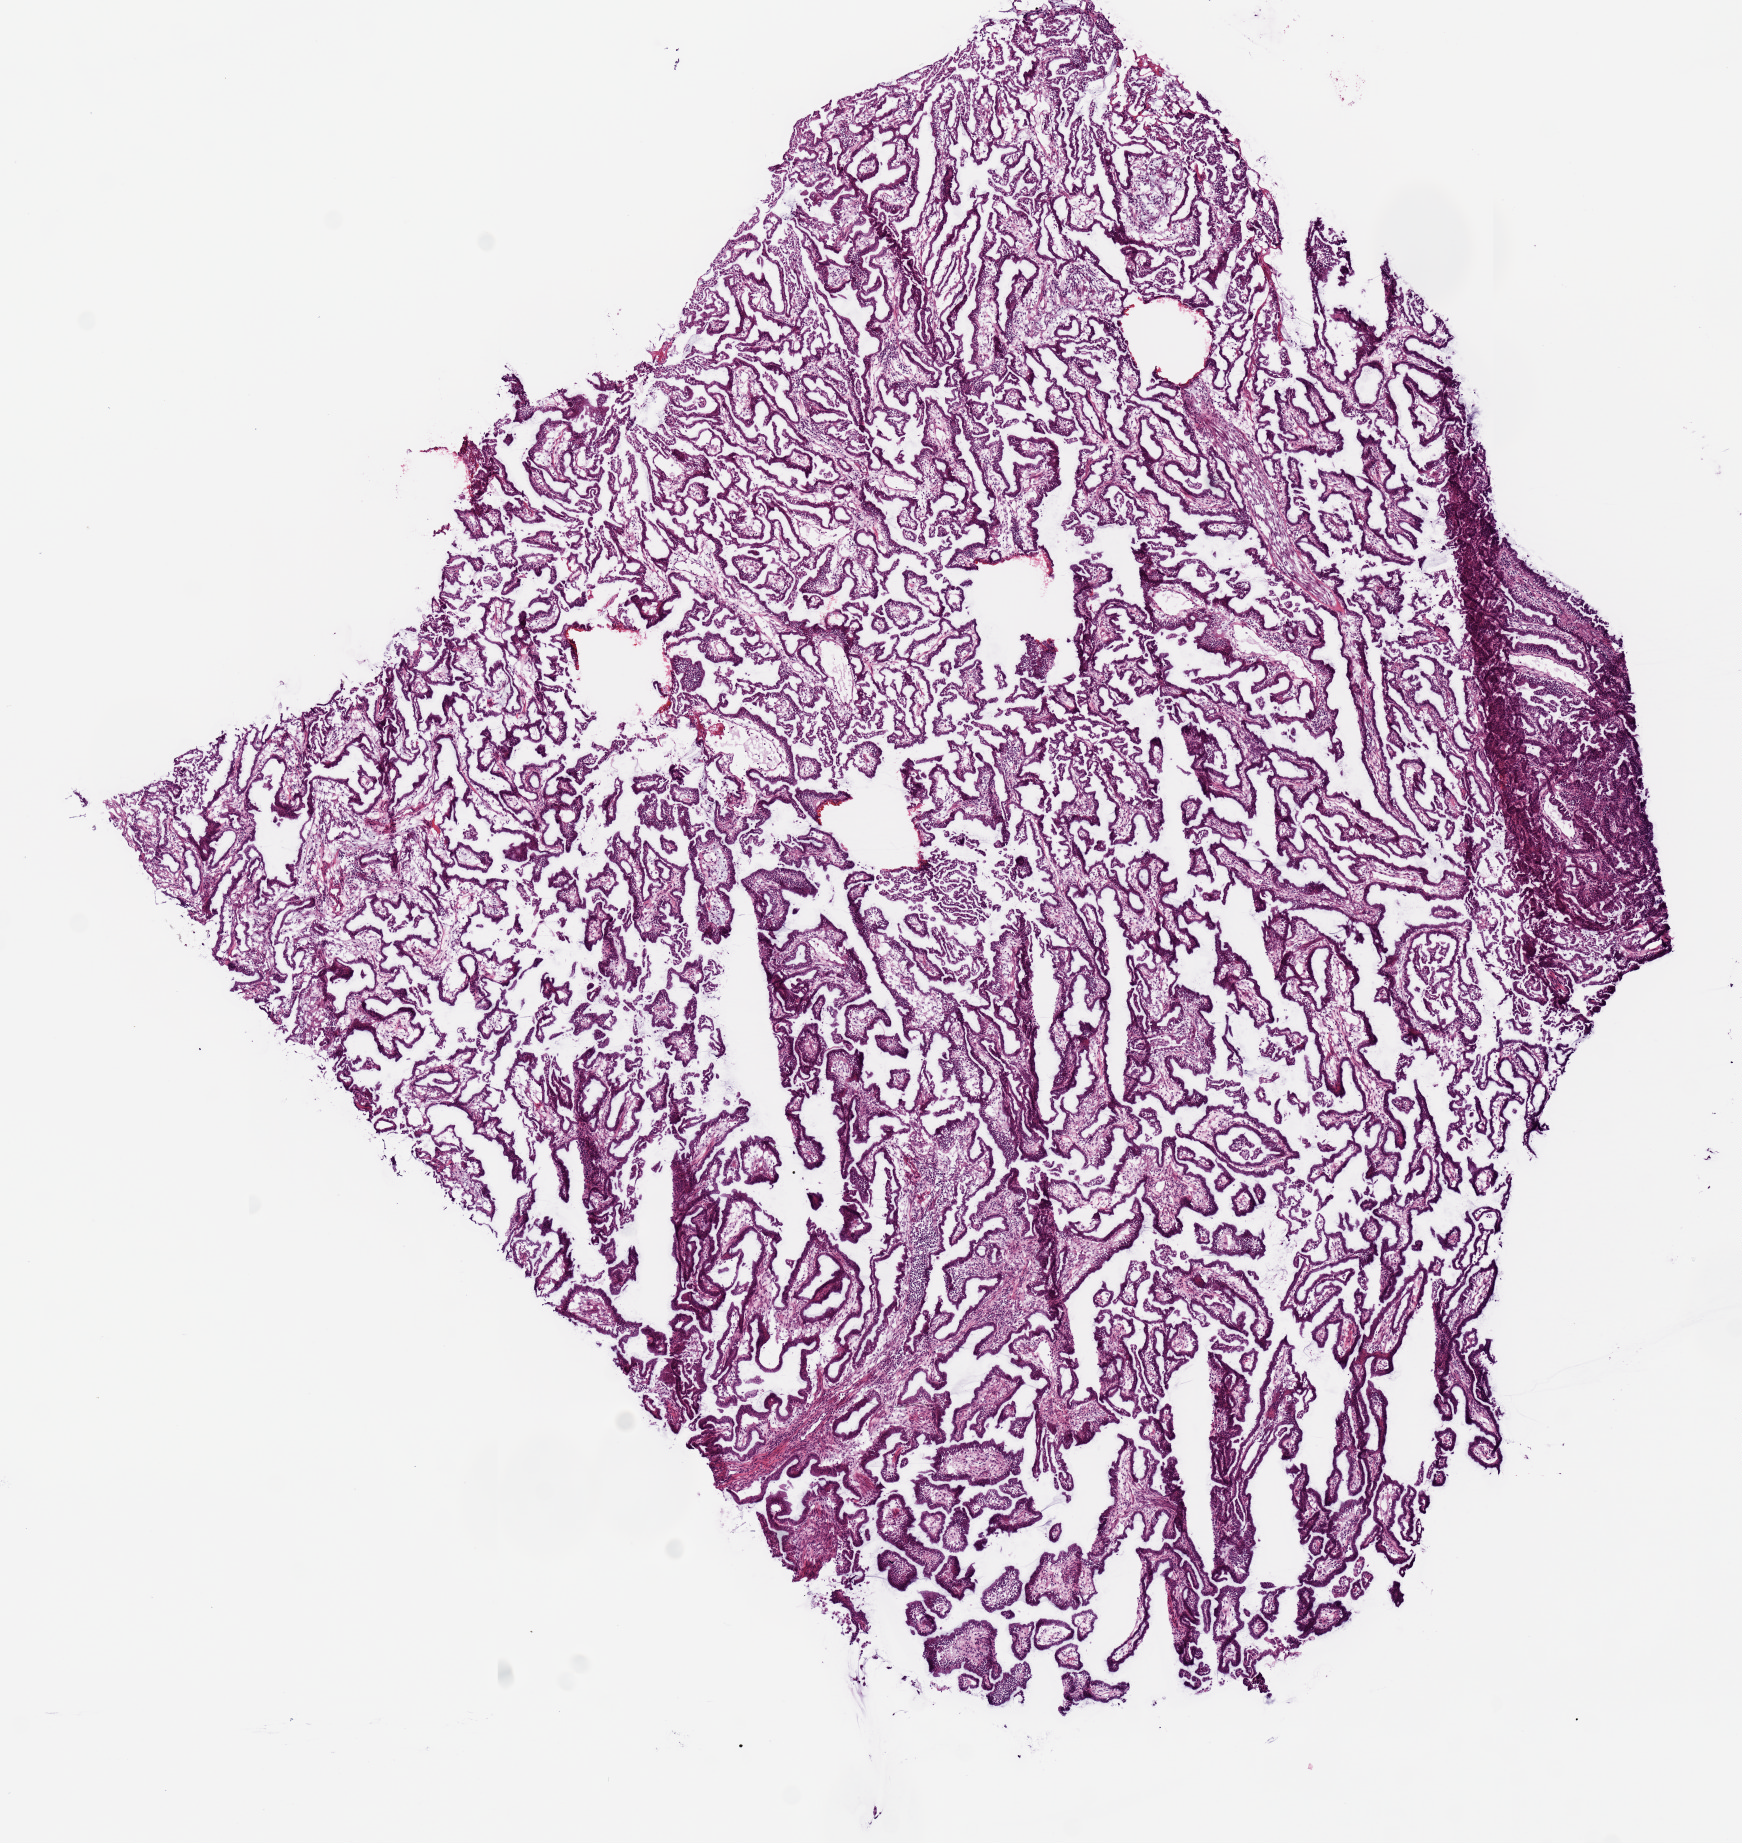
Whole-slide histology image, H&E-stained — whole scanned area (about 6.9 x 7.3 mm, acquisition: 20x scan) shown as a low-resolution overview; frozen section from the top of the tissue portion; sample: primary tumour, cervix. Female, age 55 years at initial diagnosis. Histologic grade: G2 (moderately differentiated). Slide review estimates, as recorded: tumour cells 75%, tumour nuclei 60%, normal cells 0%, stromal cells 25%, necrosis 0%. Inflammatory infiltration, as recorded: lymphocyte infiltration 0%, monocyte infiltration 0%, neutrophil infiltration 0%.
• FIGO stage: IIB
• lymph nodes positive (case pathology): 0 of 23 examined
• pathologic diagnosis: Adenocarcinoma, NOS (cervix uteri)